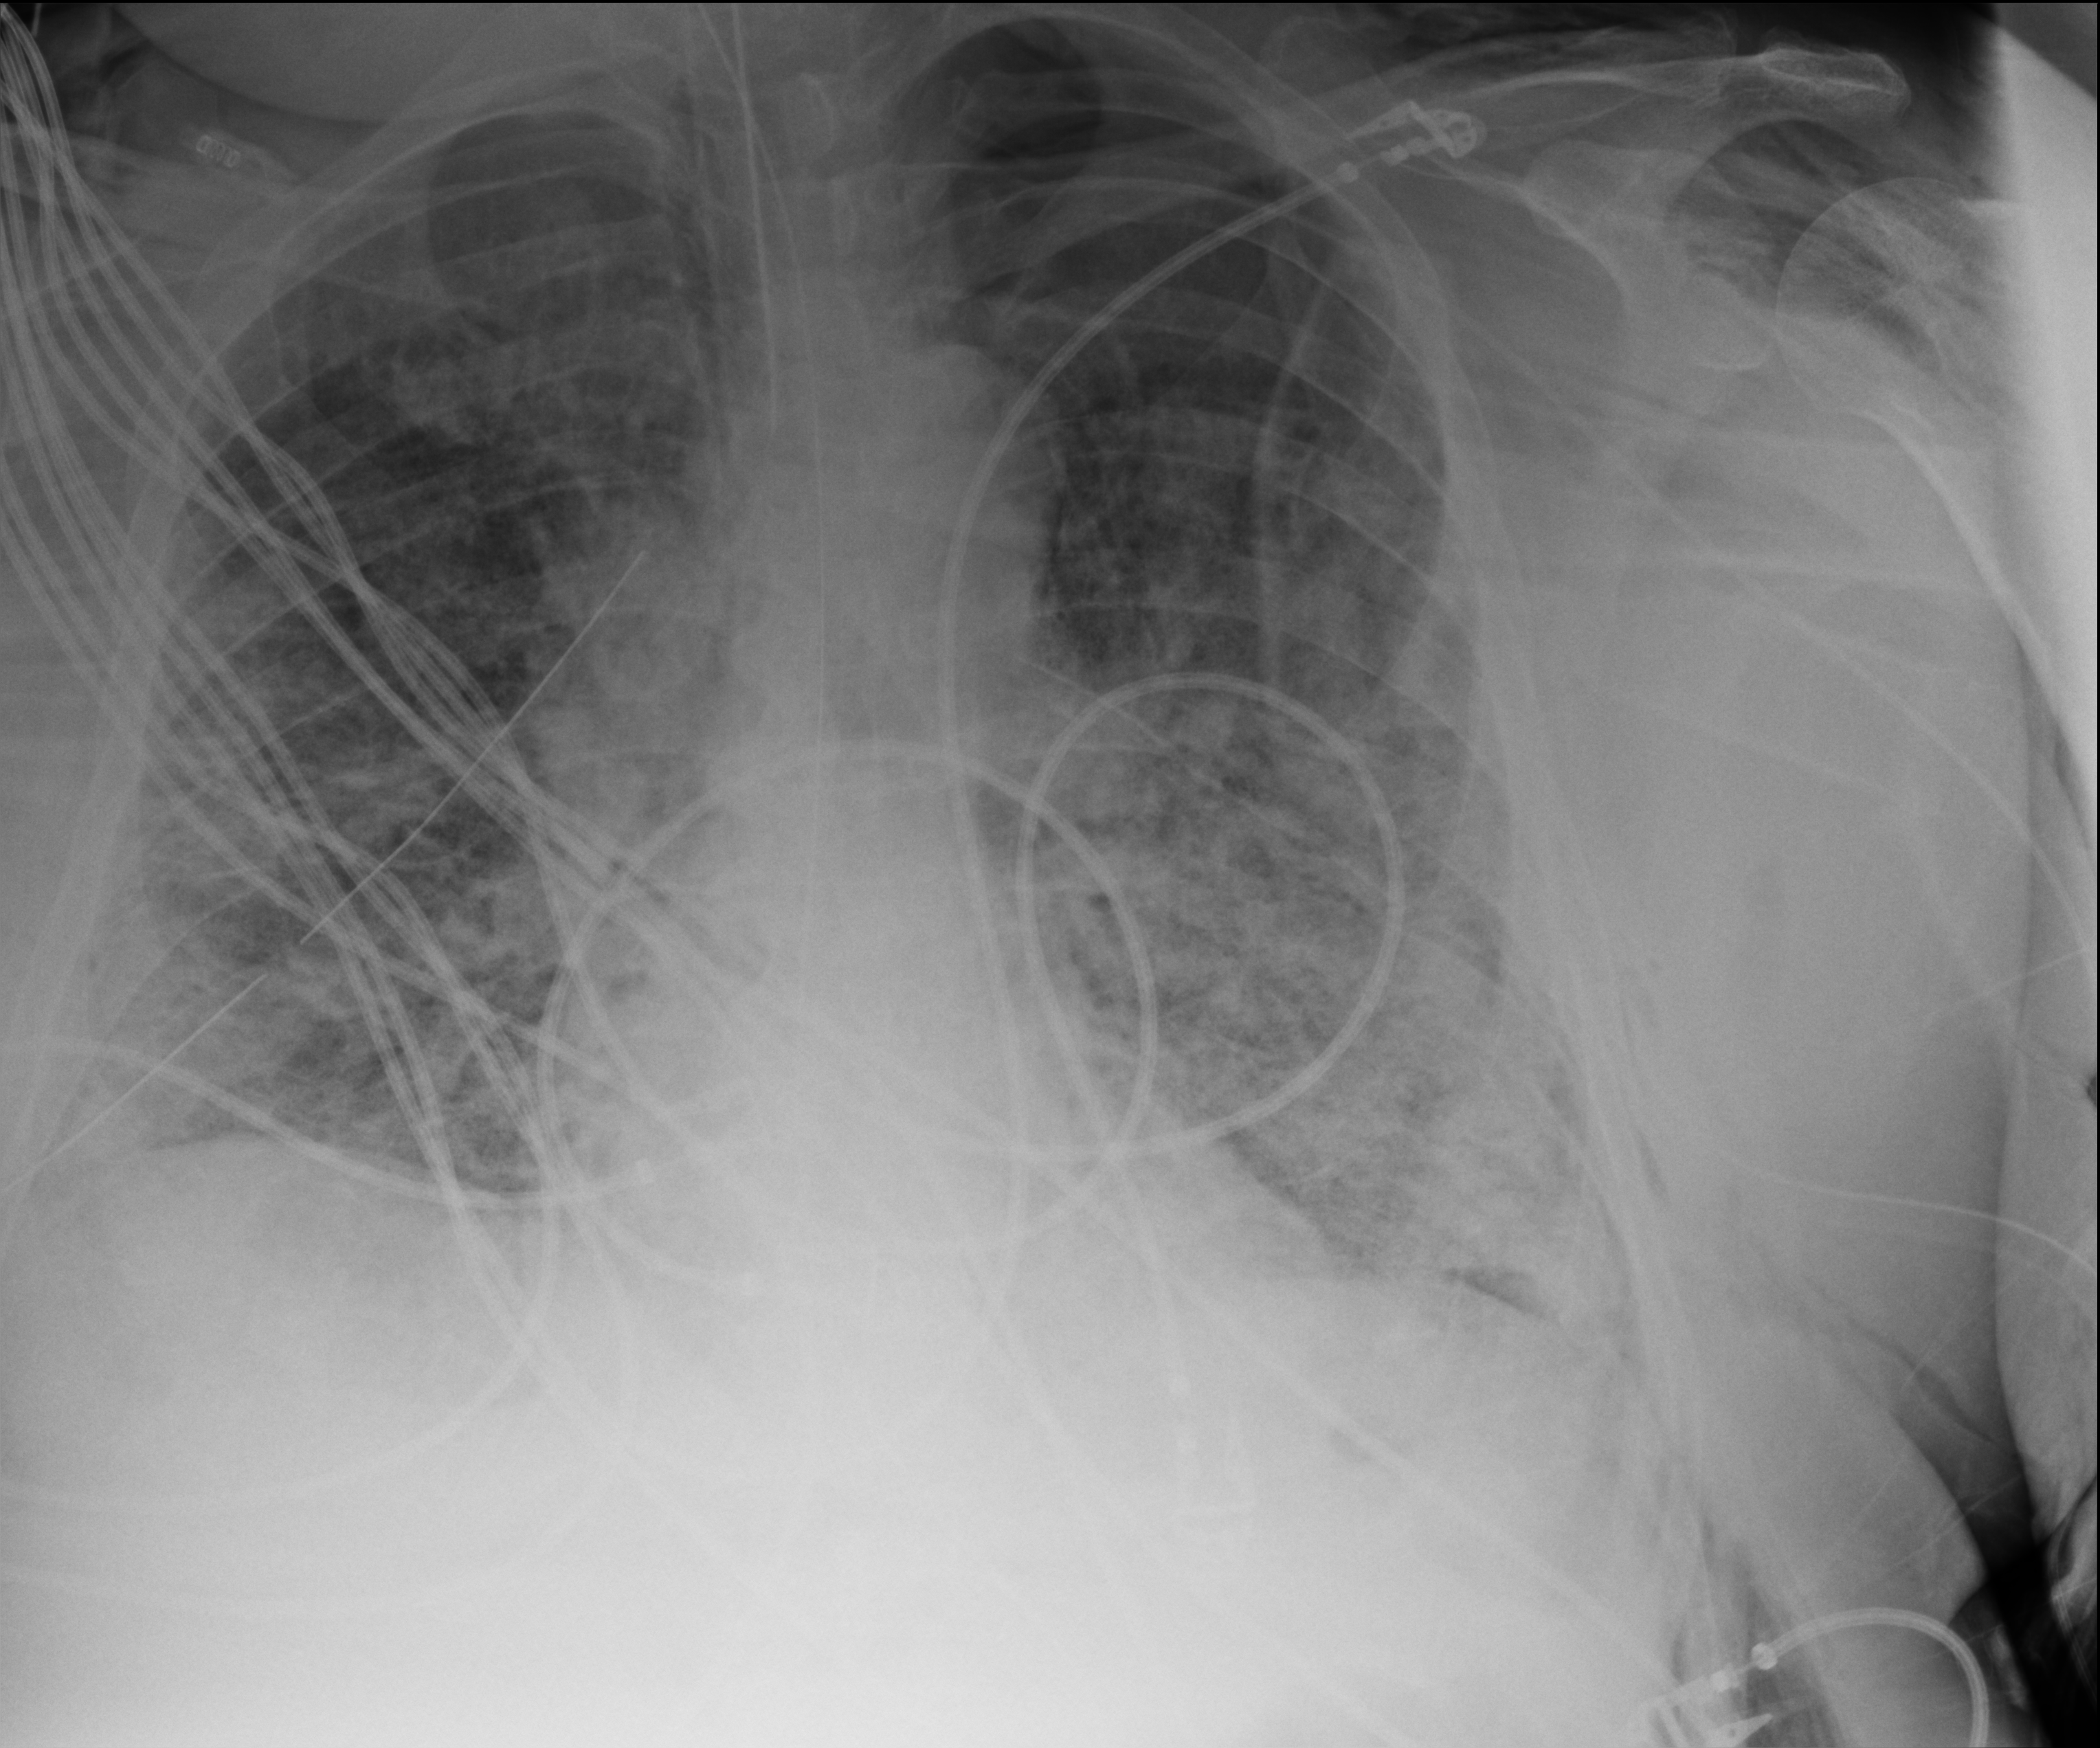
Chest X-ray (portable), anteroposterior (AP) projection. Adult patient hospitalised with COVID-19, age 18–59 years.
From the hospital-stay record, not from the radiograph (when in the stay this image was taken is not recorded): admitted to intensive care during this hospital stay: yes; other chronic lung disease (admission record): no.